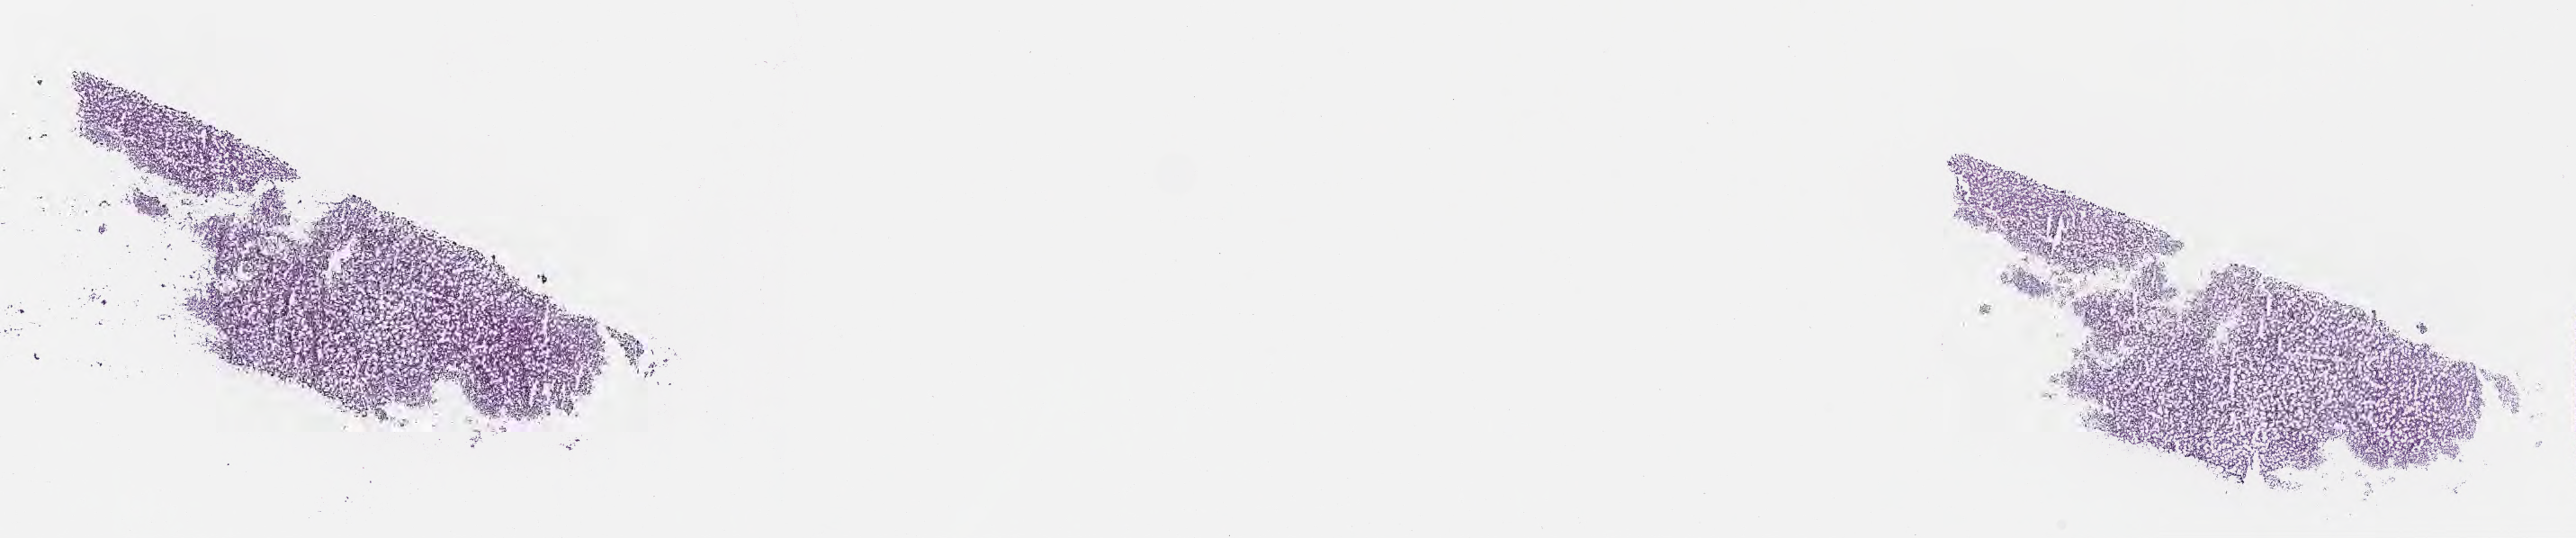
Digitized H&E-stained section, low-resolution overview of the scanned area, about 23.1 x 4.8 mm, cryosection, specimen: primary tumor, anatomic site: liver. Male, age 86 years at initial diagnosis. Tumor grade: G3 (poorly differentiated). Slide review estimates, as recorded: tumor cells 70%, tumor nuclei 70%, stromal cells 15%, necrosis 0%, normal cells 15%. Infiltration values recorded for this section: lymphocyte infiltration 0%, monocyte infiltration 0%, neutrophil infiltration 0%.
AJCC pathologic stage: Stage IIIB. Histologic diagnosis: Hepatocellular carcinoma, NOS.